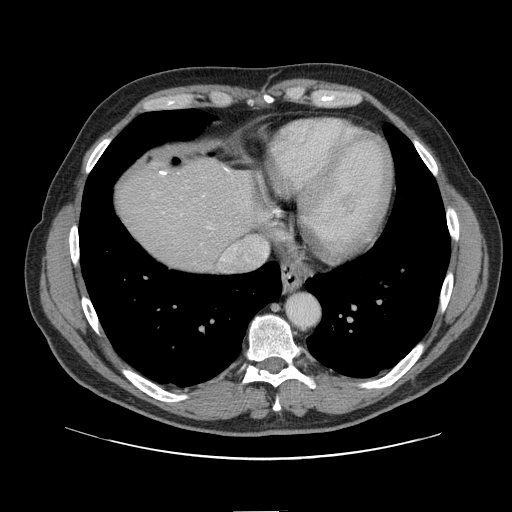
Contrast-enhanced abdominal CT, one axial slice. Intravenous contrast given. Soft-tissue window (W 400 / L 40 HU). 2.5 mm slice thickness. 512 × 512 image matrix, field of view 412 × 412 mm. Male patient, age 66 years. From the clinical record (not read from this slice): diagnosis: colorectal cancer liver metastases, imaged before liver resection; multiple liver metastases: no; largest metastasis: 3.5 cm; disease in both lobes: no.
Outlined on this slice (manually delineated by an expert):
- hepatic veins: bounding box (x1, y1, x2, y2) in pixels: (204, 195, 238, 263)
- liver: (118, 162, 254, 270)
- planned liver remnant (the part of the liver to remain after resection): (118, 162, 254, 270)